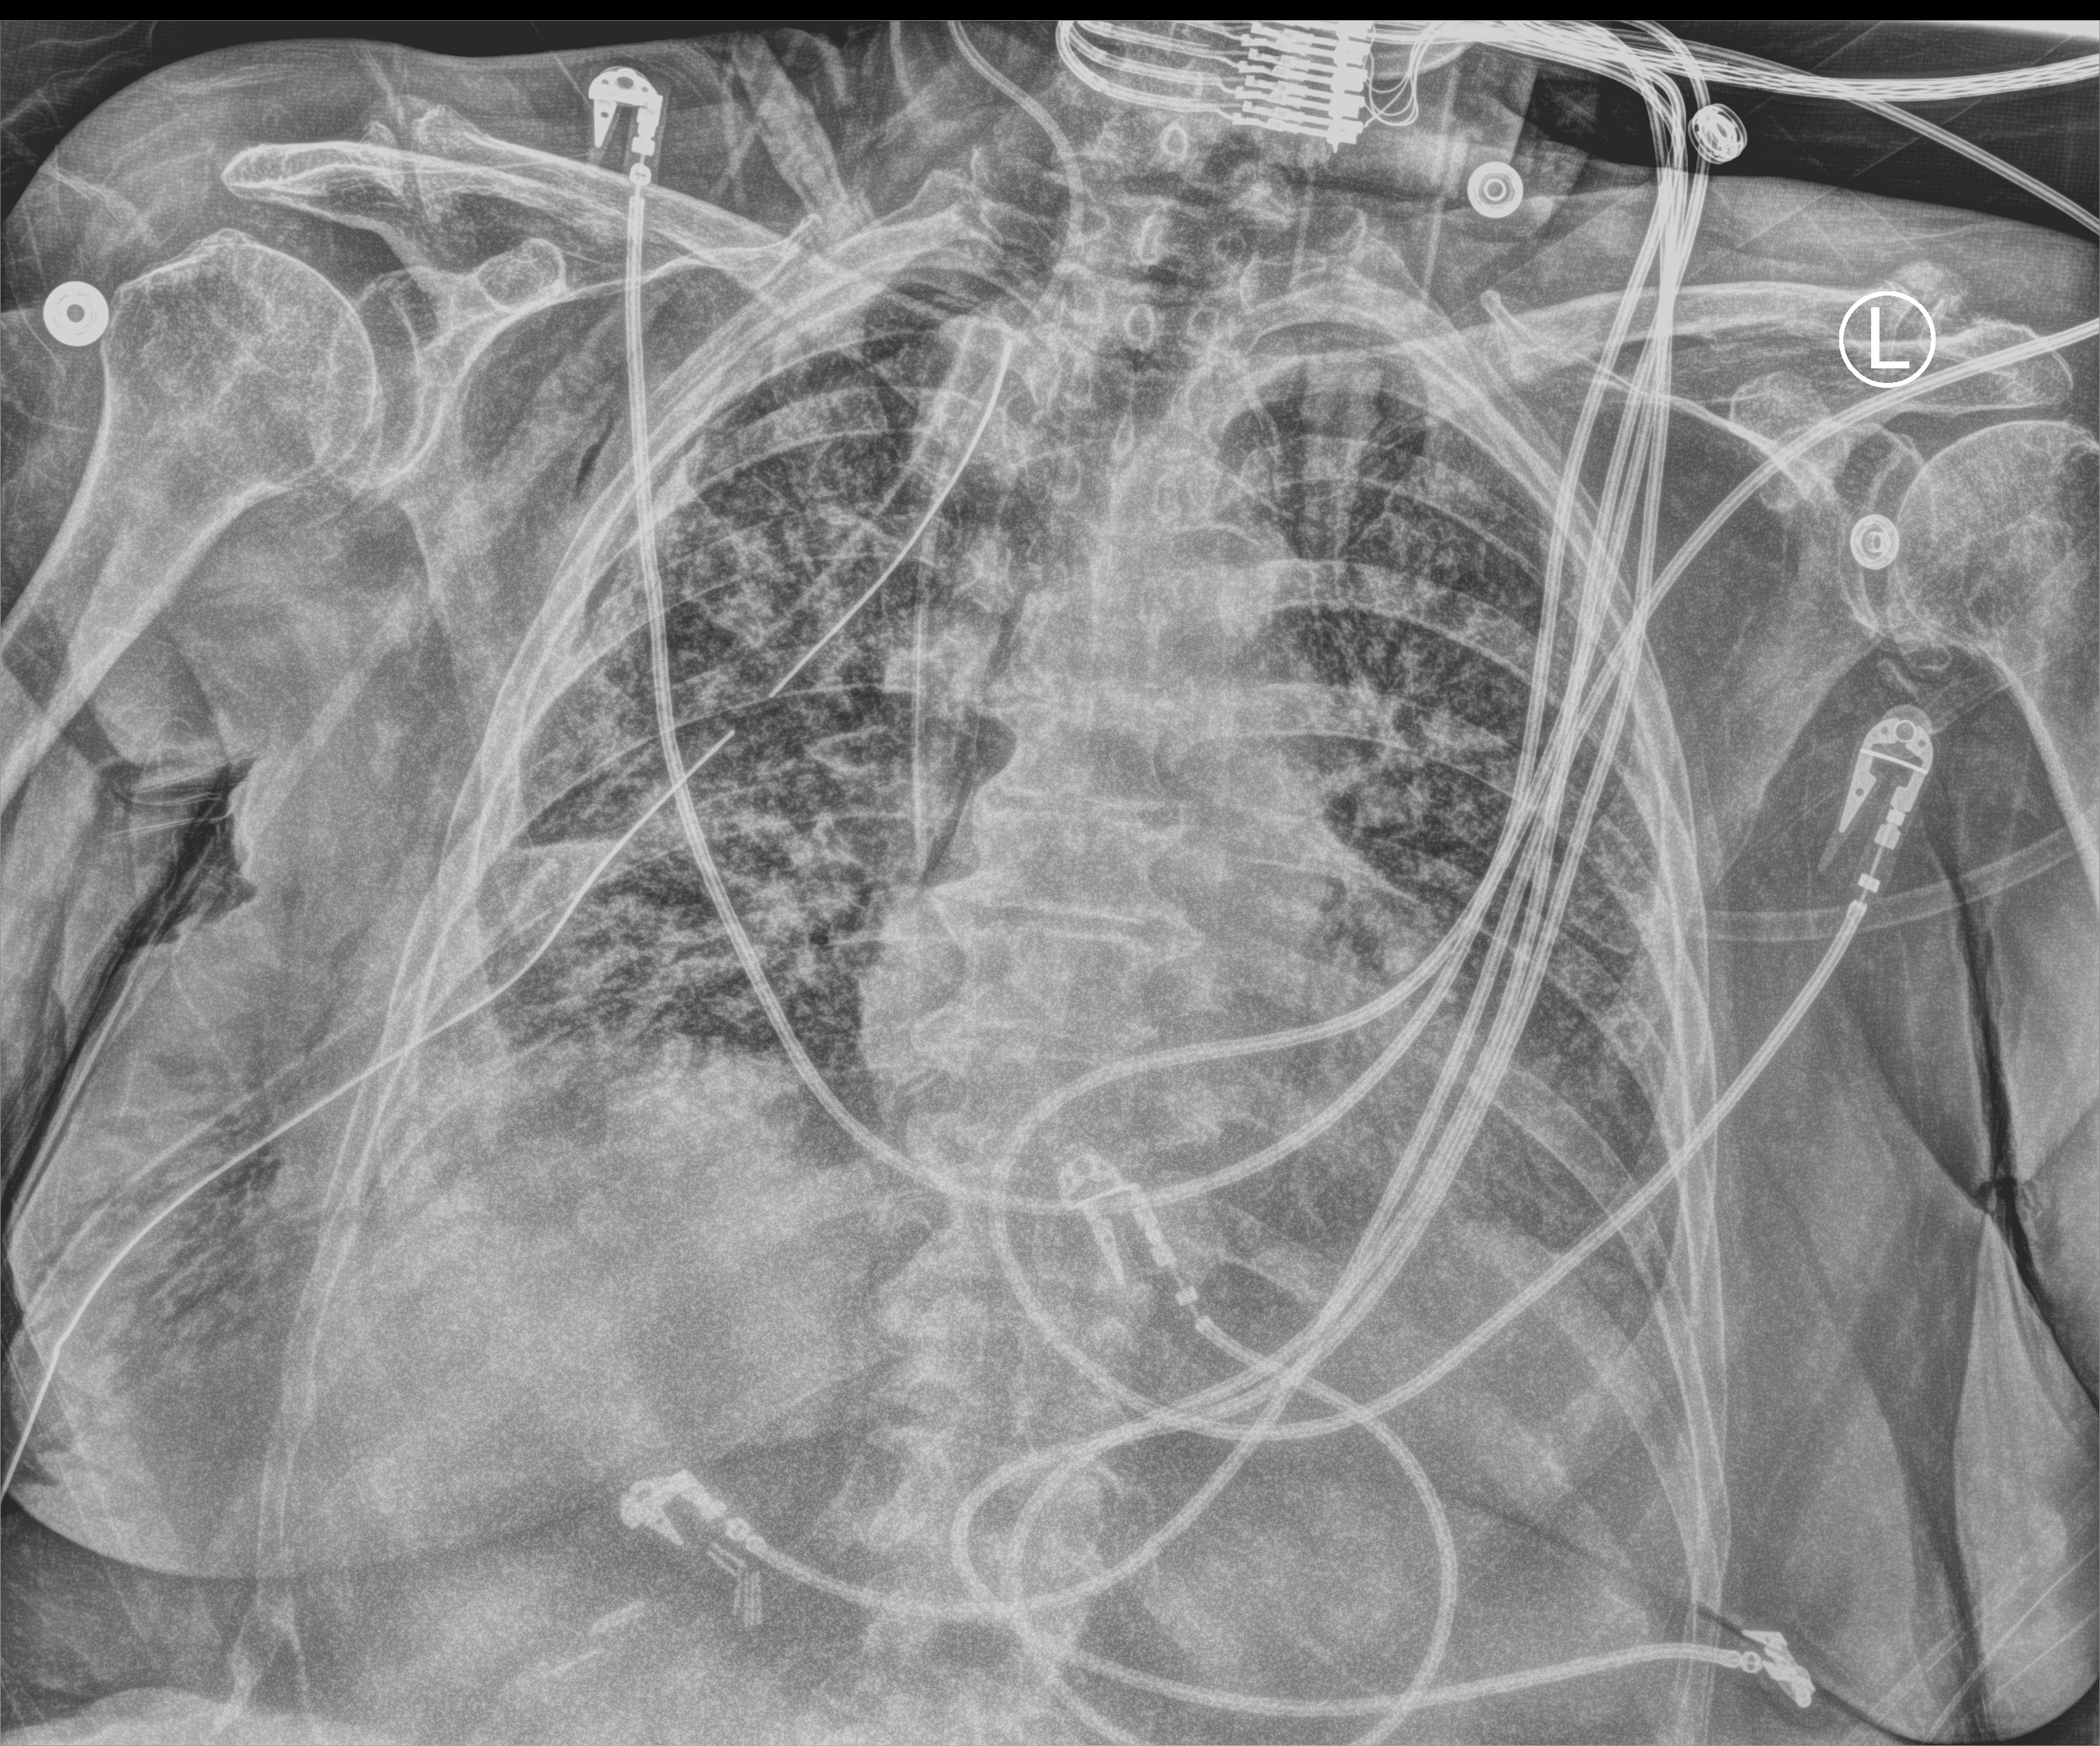
Portable chest radiograph, anteroposterior (AP) projection. Patient hospitalised with COVID-19; female, aged 75–90 years.
From the hospital-stay record, not from the radiograph (when in the stay this image was taken is not recorded): hypertension (admission record): no; smoking status (admission record): former; length of hospital stay: 56 days.